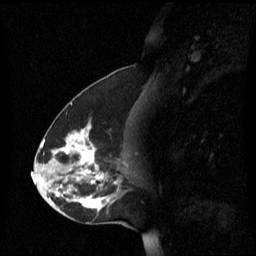
Breast MRI (dynamic contrast-enhanced), one sagittal slice; position 28 of 60 along the scan axis; dynamic contrast-enhanced series, image 2 of 3 at this slice position (ordered by acquisition); 1.5 T; TE 4.2 ms, TR 8.4 ms; 256 × 256 image matrix. Female patient, age 45 years. Case-level facts recorded for this patient, not image findings: setting: breast cancer imaged before/during neoadjuvant chemotherapy; receptor status: HR-positive, HER2-negative.
Structures marked on this image (semi-automatically segmented with operator editing):
- analysis volume of interest (the breast-tissue region the enhancement analysis was run in; not a lesion): box from (x=38, y=122) to (x=129, y=221) px
- tumour enhancement mask (voxels above the 70 % enhancement threshold inside the analysis volume of interest): (x=56, y=124)–(x=117, y=211)